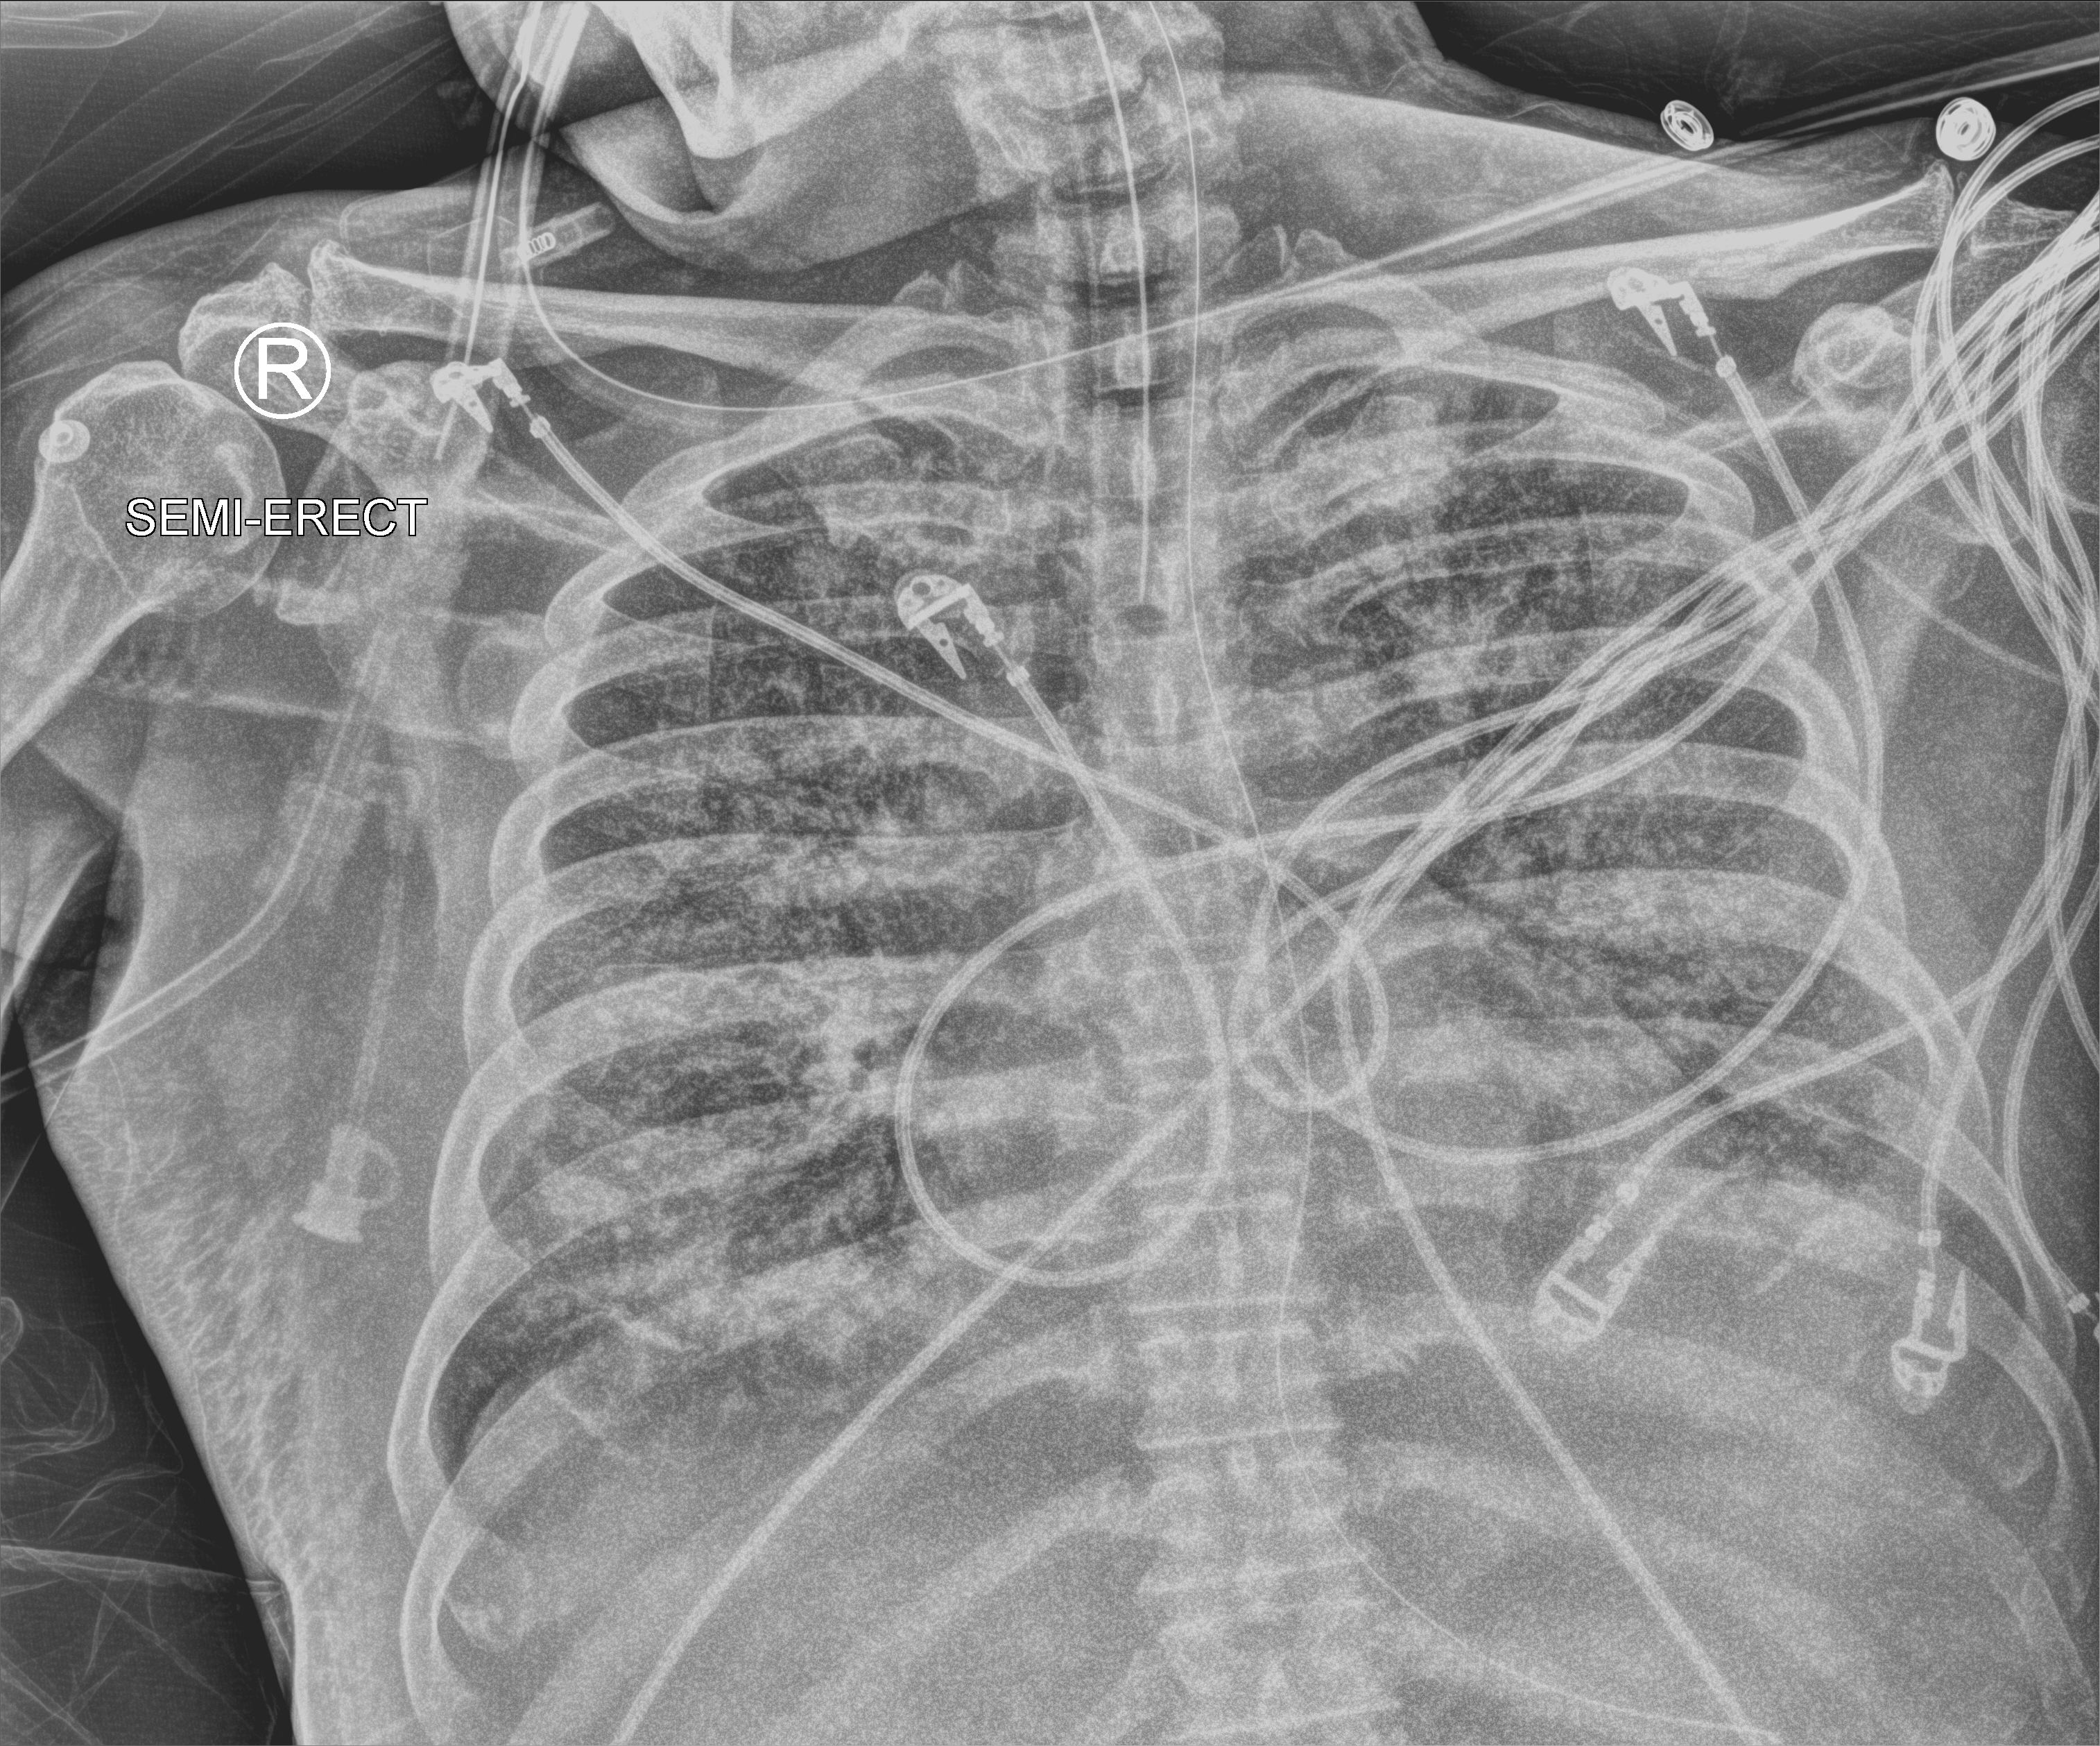
Bedside chest radiograph (computed radiography); anteroposterior (AP) projection. Male patient hospitalised with COVID-19, age 60–74 years.
Hospital-stay facts (about this admission, not read from this image; timing relative to this image not recorded): mechanically ventilated during this hospital stay: yes; hypertension (admission record): yes; COPD (admission record): no.